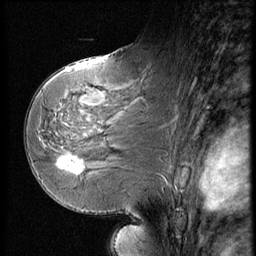
Breast MRI (dynamic contrast-enhanced), one sagittal slice; slice 30 of 56 in the series (ordered by position); dynamic contrast-enhanced series, image 2 of 3 at this slice position (ordered by acquisition); 1.5 T; TE 4.2 ms, TR 9 ms; 2.5 mm slice thickness; 256 × 256 image matrix, field of view 180 × 180 mm. Female patient, age 58 years. Case-level facts recorded for this patient, not image findings: setting: breast cancer imaged before/during neoadjuvant chemotherapy; receptor status: HR-positive, HER2-negative.
Structures marked on this image (semi-automatically segmented with operator editing):
- analysis volume of interest (the breast-tissue region the enhancement analysis was run in; not a lesion): bounding box <51,147,96,185> (left, top, right, bottom; pixels)
- tumour enhancement mask (voxels above the 140 % enhancement threshold inside the analysis volume of interest): <58,156,83,175>